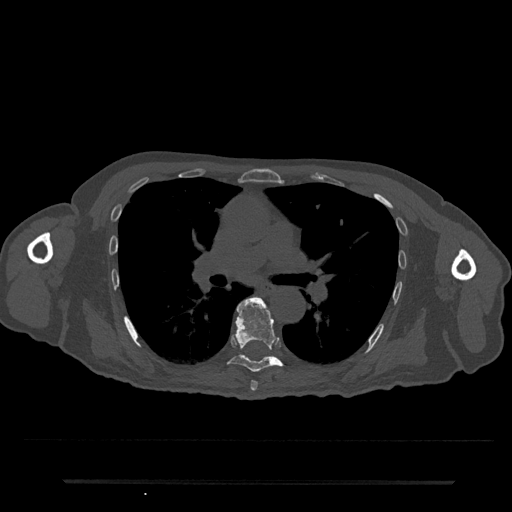
CT including the spine, one axial slice. Position 485 of 797 along the scan axis. 120 kVp. Bone window (W 1800 / L 400 HU). 0.5 mm slice thickness. 512 × 512 image matrix, field of view 427 × 427 mm. Male patient, age 74 years. From the clinical record (not read from this slice): primary cancer: prostate.
Outlined on this slice (semi-automatically segmented with operator editing):
- T6 vertebra: box from (x=250, y=380) to (x=258, y=391) px
- T7 vertebra: (x=228, y=297)–(x=283, y=372)